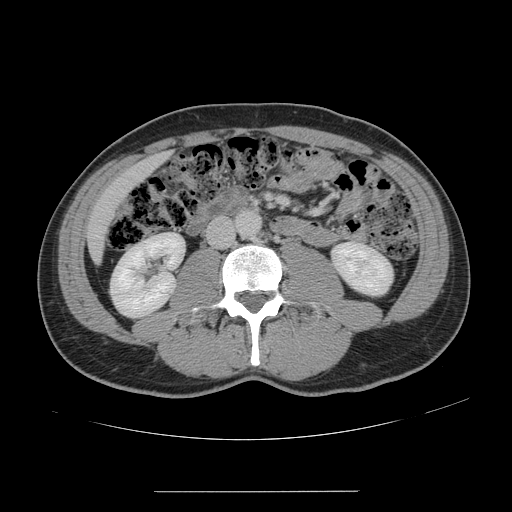
Contrast-enhanced abdominal CT, one axial slice; intravenous contrast given; soft-tissue window (W 400 / L 40 HU); 2.5 mm slice thickness; 512 × 512 image matrix, field of view 401 × 401 mm. Male patient, age 53 years. Case-level facts recorded for this patient, not image findings: diagnosis: colorectal cancer liver metastases, imaged before liver resection; multiple liver metastases: yes; largest metastasis: 2.4 cm; disease in both lobes: no.
Outlined on this slice (manually delineated by an expert):
- liver: bounding box (x1, y1, x2, y2) in pixels: (89, 156, 165, 260)